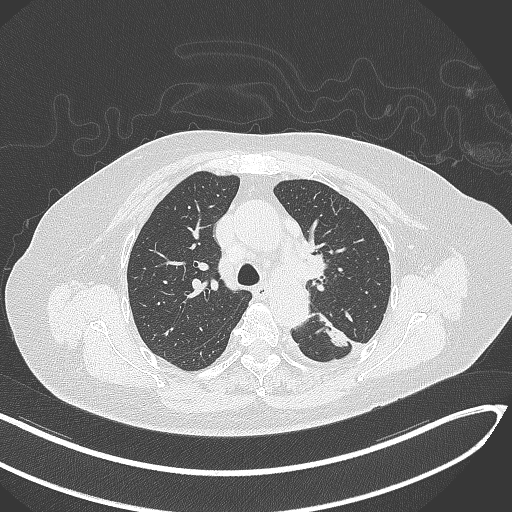
Chest CT, one axial slice. Position 218 of 270 along the scan axis. 120 kVp. Lung window (W 1500 / L -600 HU). 1 mm slice thickness. 512 × 512 image matrix, field of view 400 × 400 mm. Patient: female, 76 years. From the clinical record (not read from this slice): clinical TNM (as recorded): T1c N0 M0.
Outlined on this slice (rectangle marked by the reading radiologist):
- lung tumour (recorded histology: adenocarcinoma): box from (x=316, y=307) to (x=352, y=355) px